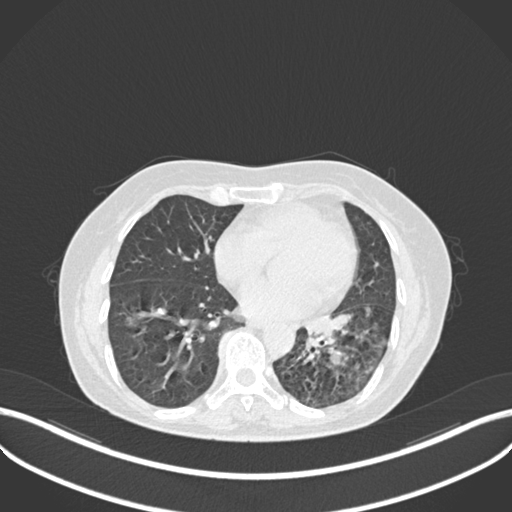
Chest CT, one axial slice; position 105 of 270 along the scan axis; reconstruction kernel B30f; 120 kVp; lung window (W 1500 / L -600 HU); 1 mm slice thickness; 512 × 512 image matrix. Patient: female, 63 years. Case-level facts recorded for this patient, not image findings: clinical TNM (as recorded): T1b N0 M0.
Annotated regions visible in this slice (rectangle marked by the reading radiologist):
- lung tumour (recorded histology: adenocarcinoma): bounding box <305,309,358,345> (left, top, right, bottom; pixels)